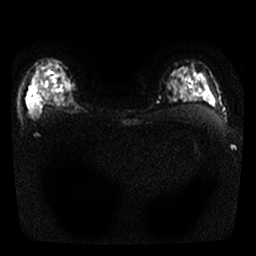
Breast MRI, one axial slice; slice 20 of 25 in the series (ordered by position); diffusion-weighted series; image 2 of 4 stored at this slice position (different b-values; order by instance number); 1.5 T; 4 mm slice thickness; 256 × 256 image matrix, field of view 300 × 300 mm. Female patient.
Structures marked on this image (manually delineated by an expert):
- tumour on diffusion-weighted imaging: bounding box (x1, y1, x2, y2) in pixels: (28, 79, 70, 118)